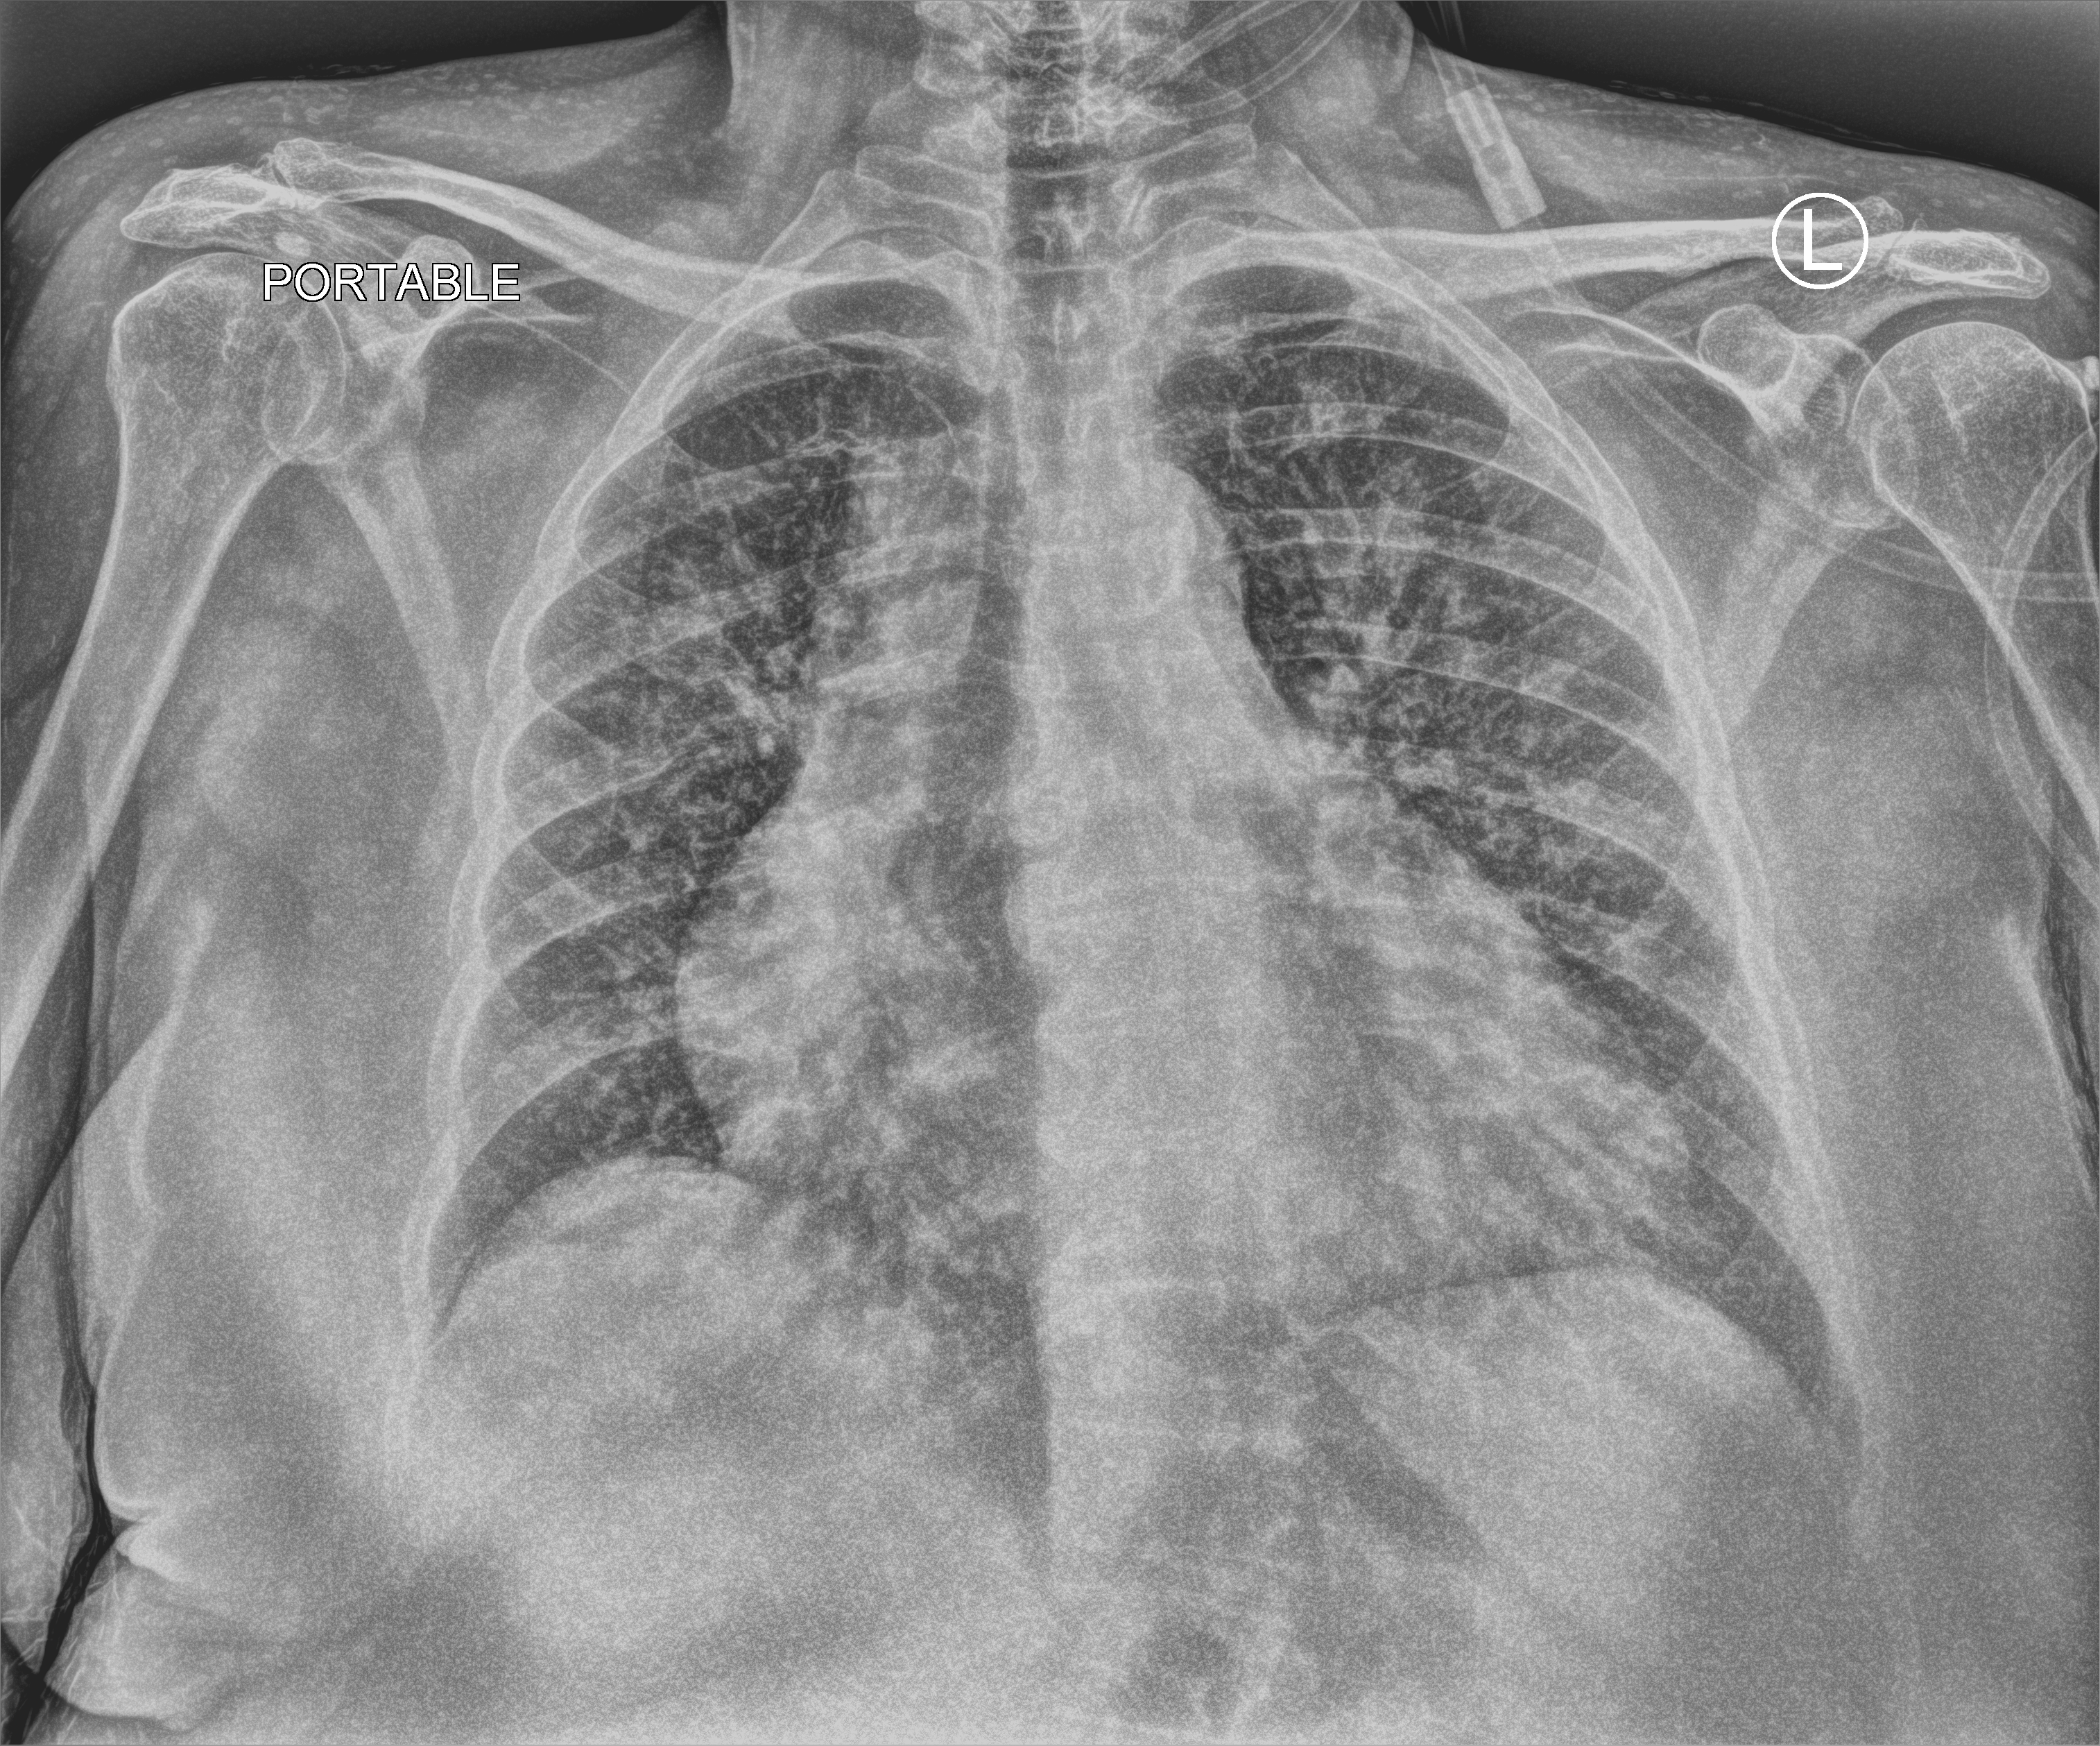
Chest X-ray (portable), anteroposterior (AP) projection. Female patient hospitalised with COVID-19, age 75–90 years.
From the hospital-stay record, not from the radiograph (when in the stay this image was taken is not recorded): admitted to intensive care during this hospital stay: yes; diabetes (admission record): no.